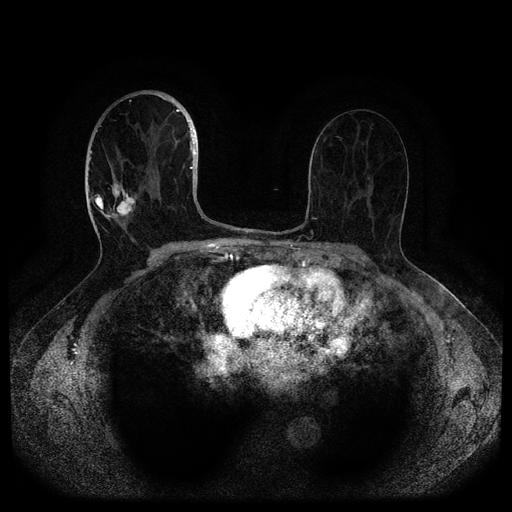
Breast MRI (dynamic contrast-enhanced, multi-phase), one axial slice; position 55 of 116 along the scan axis; dynamic contrast-enhanced series, time point 2 of 5 at this slice position (early post-contrast); 1.5 T; TE 2.6 ms, TR 5.3 ms; 512 × 512 image matrix, field of view 350 × 350 mm. Patient: female, 82 years.
Annotated regions visible in this slice (semi-automatically segmented with operator editing):
- breast lesion (labelled 'tumour' in the annotation; benign lesions carry a separate 'benign' label): bounding box (x1, y1, x2, y2) in pixels: (108, 179, 136, 221)